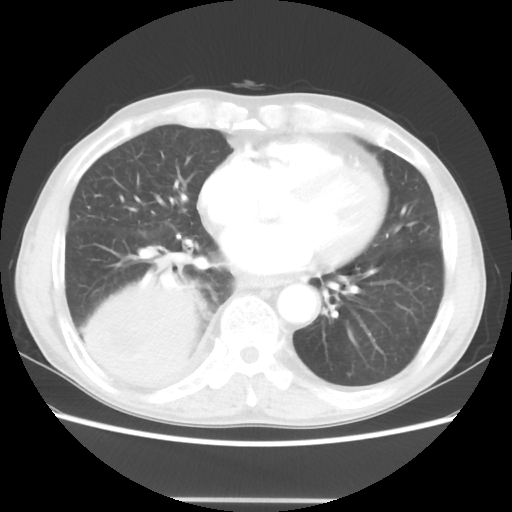
Chest CT, one axial slice; position 16 of 48 along the scan axis; reconstruction kernel STANDARD; lung window (W 1500 / L -600 HU); 512 × 512 image matrix, field of view 361 × 361 mm. Patient: male, 66 years. From the clinical record (not read from this slice): clinical TNM (as recorded): T4 N1 M1.
Structures marked on this image (bounding box drawn by a radiologist):
- lung tumour (recorded histology: small cell carcinoma): box from (x=72, y=261) to (x=213, y=403) px